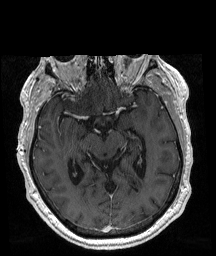
Brain MRI from a brain-tumour surgery series, one axial slice. Position 113 of 192 along the scan axis. T1-weighted post-contrast. 216 × 256 image matrix. From the clinical record (not read from this slice): histopathology: Glioblastoma; WHO grade: 4; IDH mutation: no; tumour location: Right Frontal.
Structures marked on this image (manually delineated by an expert):
- tumour: bounding box [x1, y1, x2, y2] px = [66, 92, 69, 95]